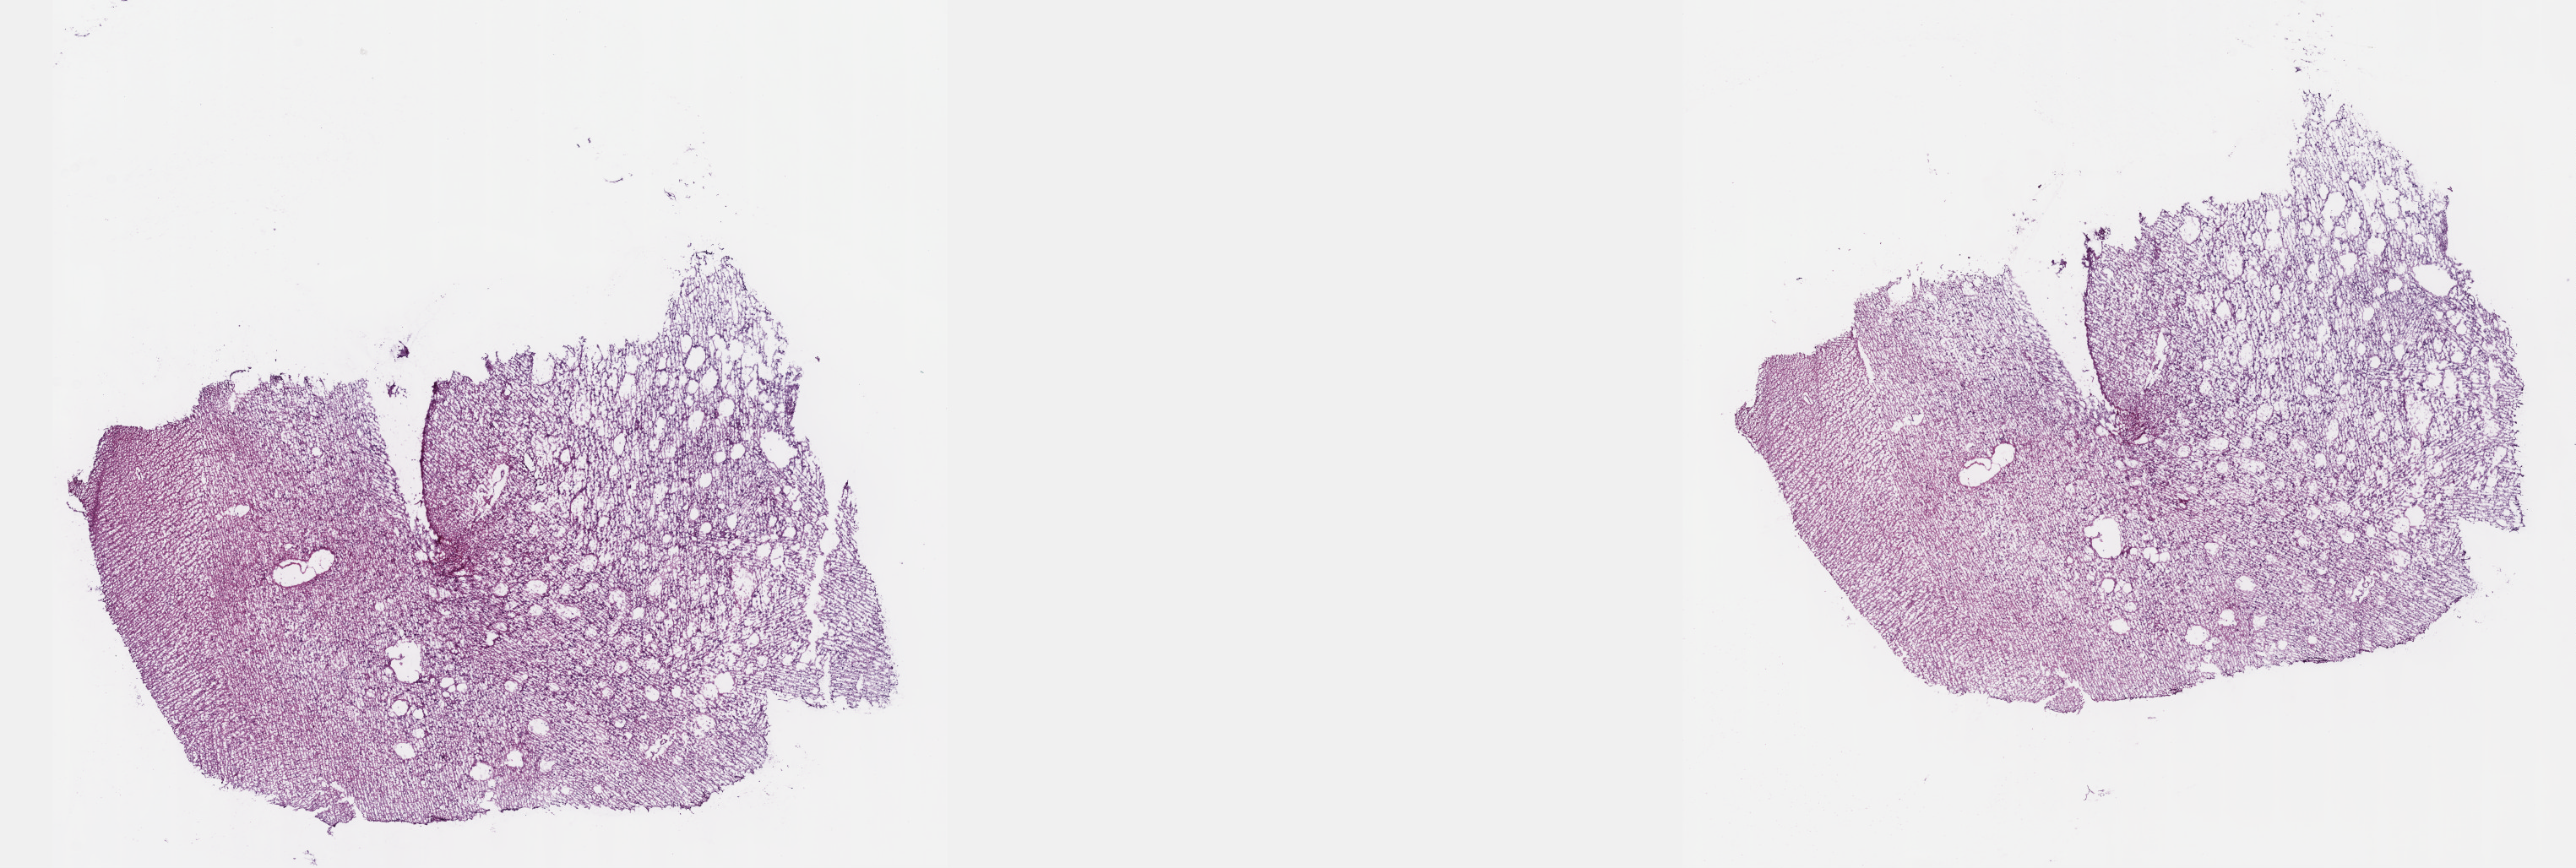
Whole-slide histology image, H&E-stained, whole scanned area (about 24.6 x 8.3 mm, slide scanned at 40x) shown as a low-resolution overview. Frozen section. Brain, primary tumour sample. Female, age 41 years at initial diagnosis. Histologic grade: G2 (moderately differentiated). Composition of this section per pathologist review: tumour cells 30%, tumour nuclei 75%, normal cells 10%, stromal cells 60%, necrosis 0%. Infiltration values recorded for this section: lymphocyte infiltration 0%, monocyte infiltration 0%, neutrophil infiltration 0%.
* laterality: right
* histologic diagnosis: Astrocytoma, NOS (cerebrum)